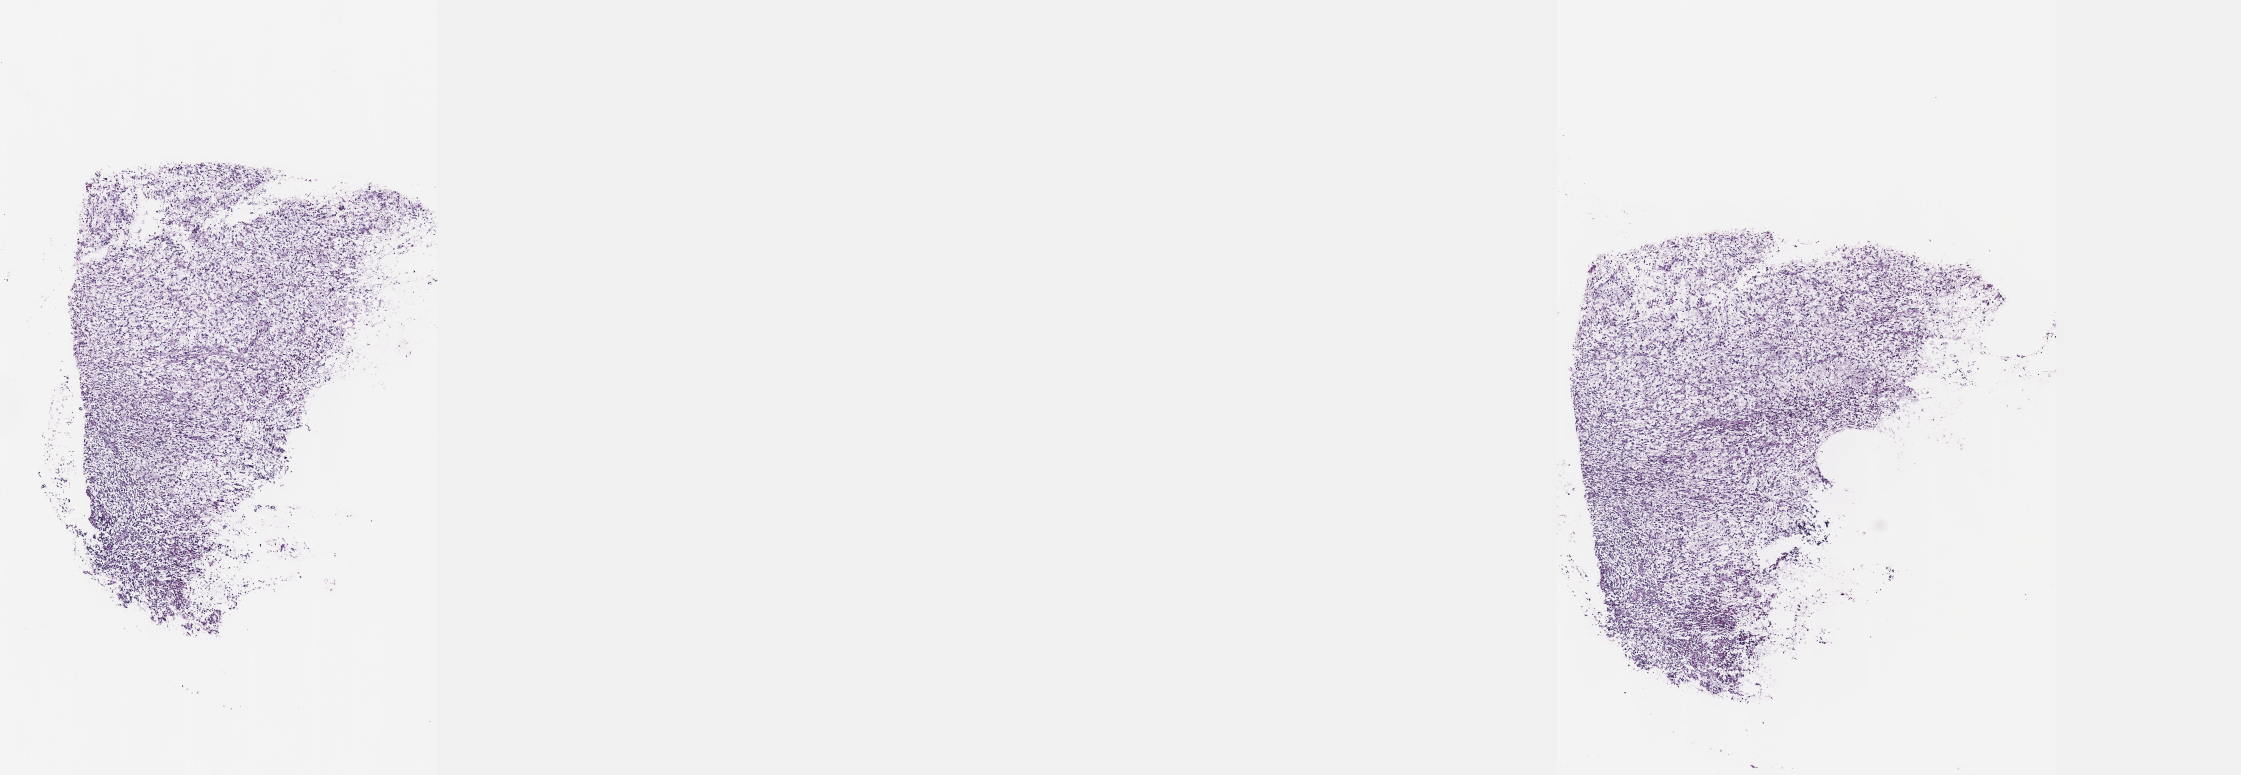
H&E-stained whole-slide image, a low-resolution overview of the entire scanned area, about 18.1 x 6.3 mm (slide scanned at 40x), frozen section, sample: primary tumour, brain. Female, age 41 years at initial diagnosis. Pathologist review of this section (percent, as recorded): tumour cells 80%, tumour nuclei 90%.
Pathologic diagnosis: Mixed glioma (cerebrum).